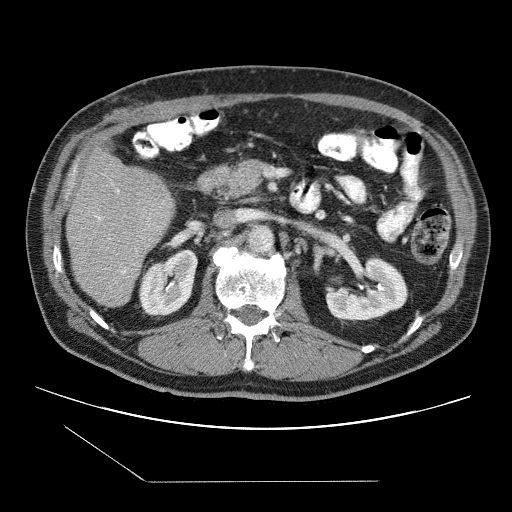
Contrast-enhanced abdominal CT (liver protocol), one axial slice; 120 kVp; one of 2 acquisitions stored at this slice position; soft-tissue window (W 400 / L 40 HU); 2.5 mm slice thickness; 512 × 512 image matrix, field of view 400 × 400 mm. From the clinical record (not read from this slice): diagnosis: hepatocellular carcinoma (patient treated with transarterial chemoembolisation; whether this scan precedes or follows treatment is not stated here); TNM stage (as recorded): Stage-IIIB; Child-Pugh class: A; tumour differentiation: well differentiated; tumour nodularity: multinodular.
Structures marked on this image (semi-automatically segmented with operator editing):
- liver parenchyma outside the tumour (the mass and vessels are separate outlines, so this box may not span the whole liver): bounding box [x1, y1, x2, y2] px = [66, 150, 174, 306]
- liver vessels: [97, 190, 126, 274]